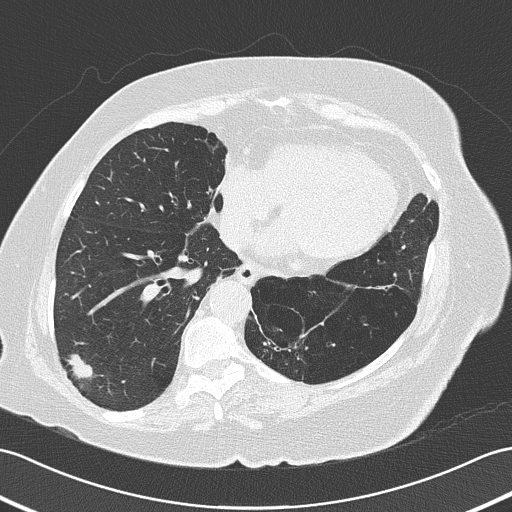
Axial slice from a low-dose chest CT screening exam; baseline screening round; lung window (W 1500 / L -600 HU); 2 mm slice thickness; lung (sharp) reconstruction kernel (B50f); 120 kVp. Female participant, aged 73 years at enrolment. Former smoker at enrolment.
Expert reader's lesion annotation, bounding box [x1, y1, x2, y2] px = [55, 339, 101, 387]. The screening reader recorded 4 non-calcified nodules or masses ≥4 mm on this exam; which of them this box marks is not recorded. Later outcome: lung cancer diagnosed 50 days after this screen — adenocarcinoma, NOS, right lower lobe, poorly differentiated (G3), stage IB (AJCC 6th edition), 17 mm at pathology.